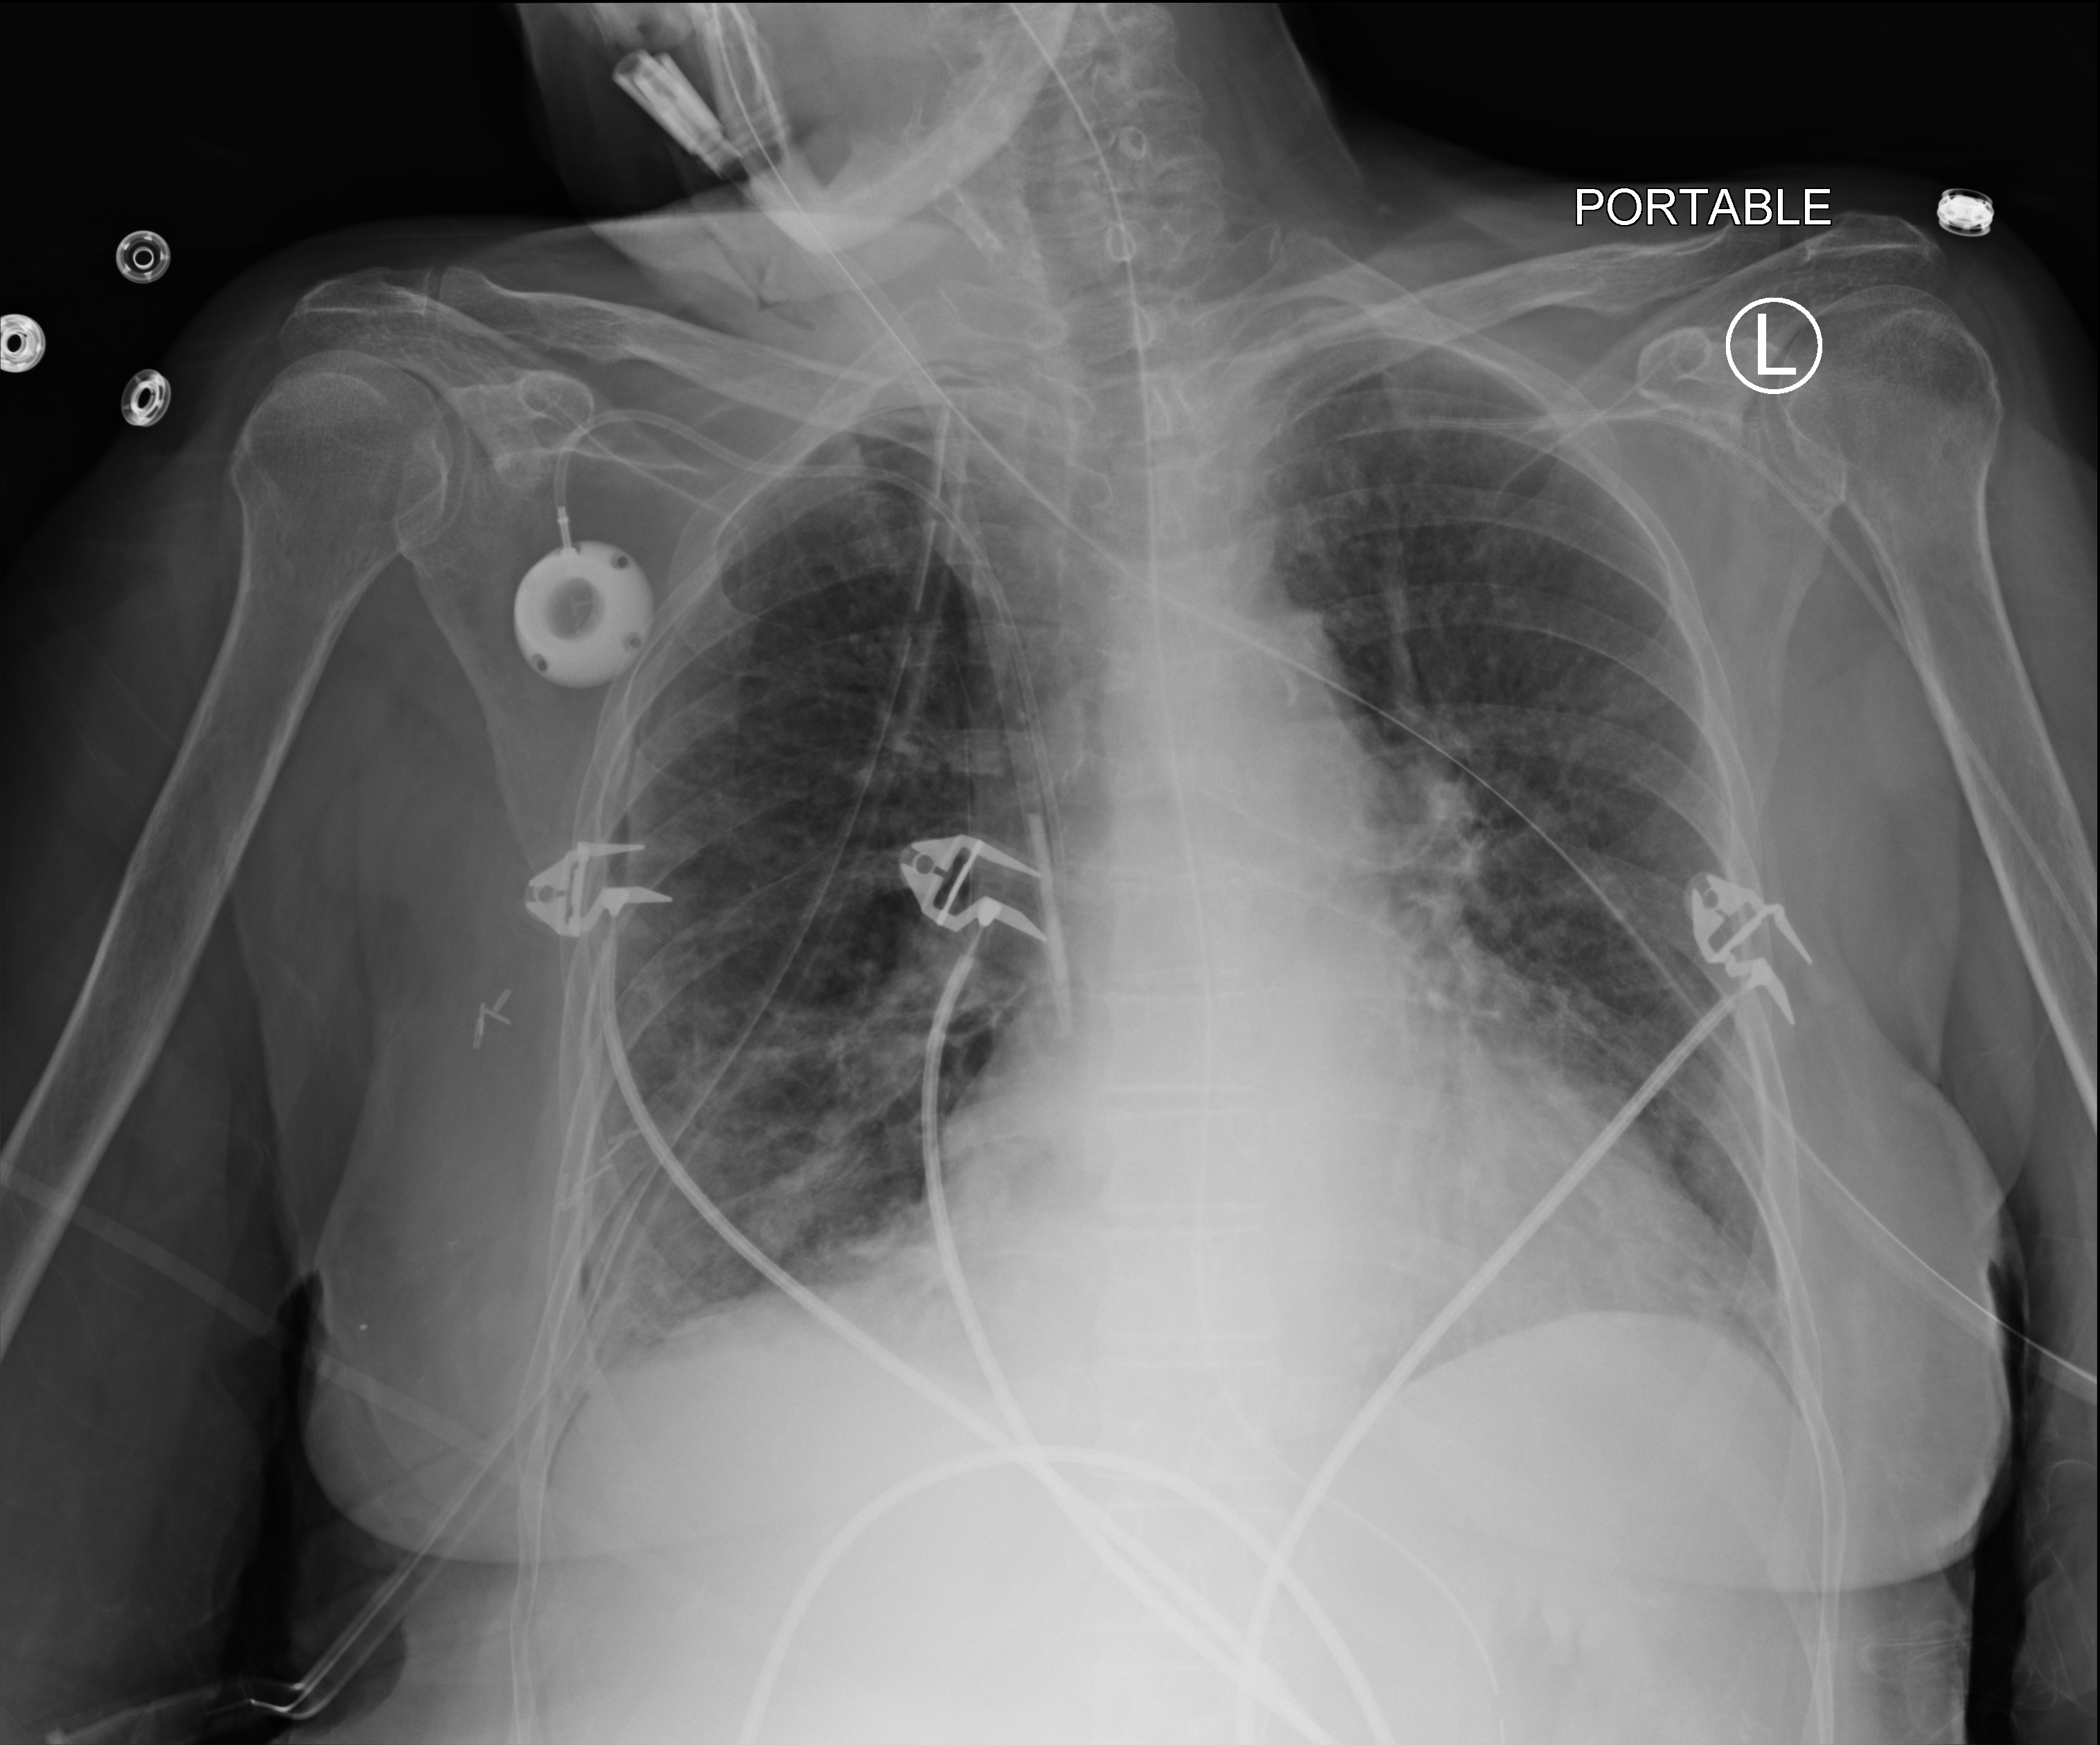
Chest X-ray (portable), anteroposterior (AP) projection. Female patient hospitalised with COVID-19, age 60–74 years.
Hospital-stay facts (about this admission, not read from this image; timing relative to this image not recorded):
- admitted to intensive care during this hospital stay: yes